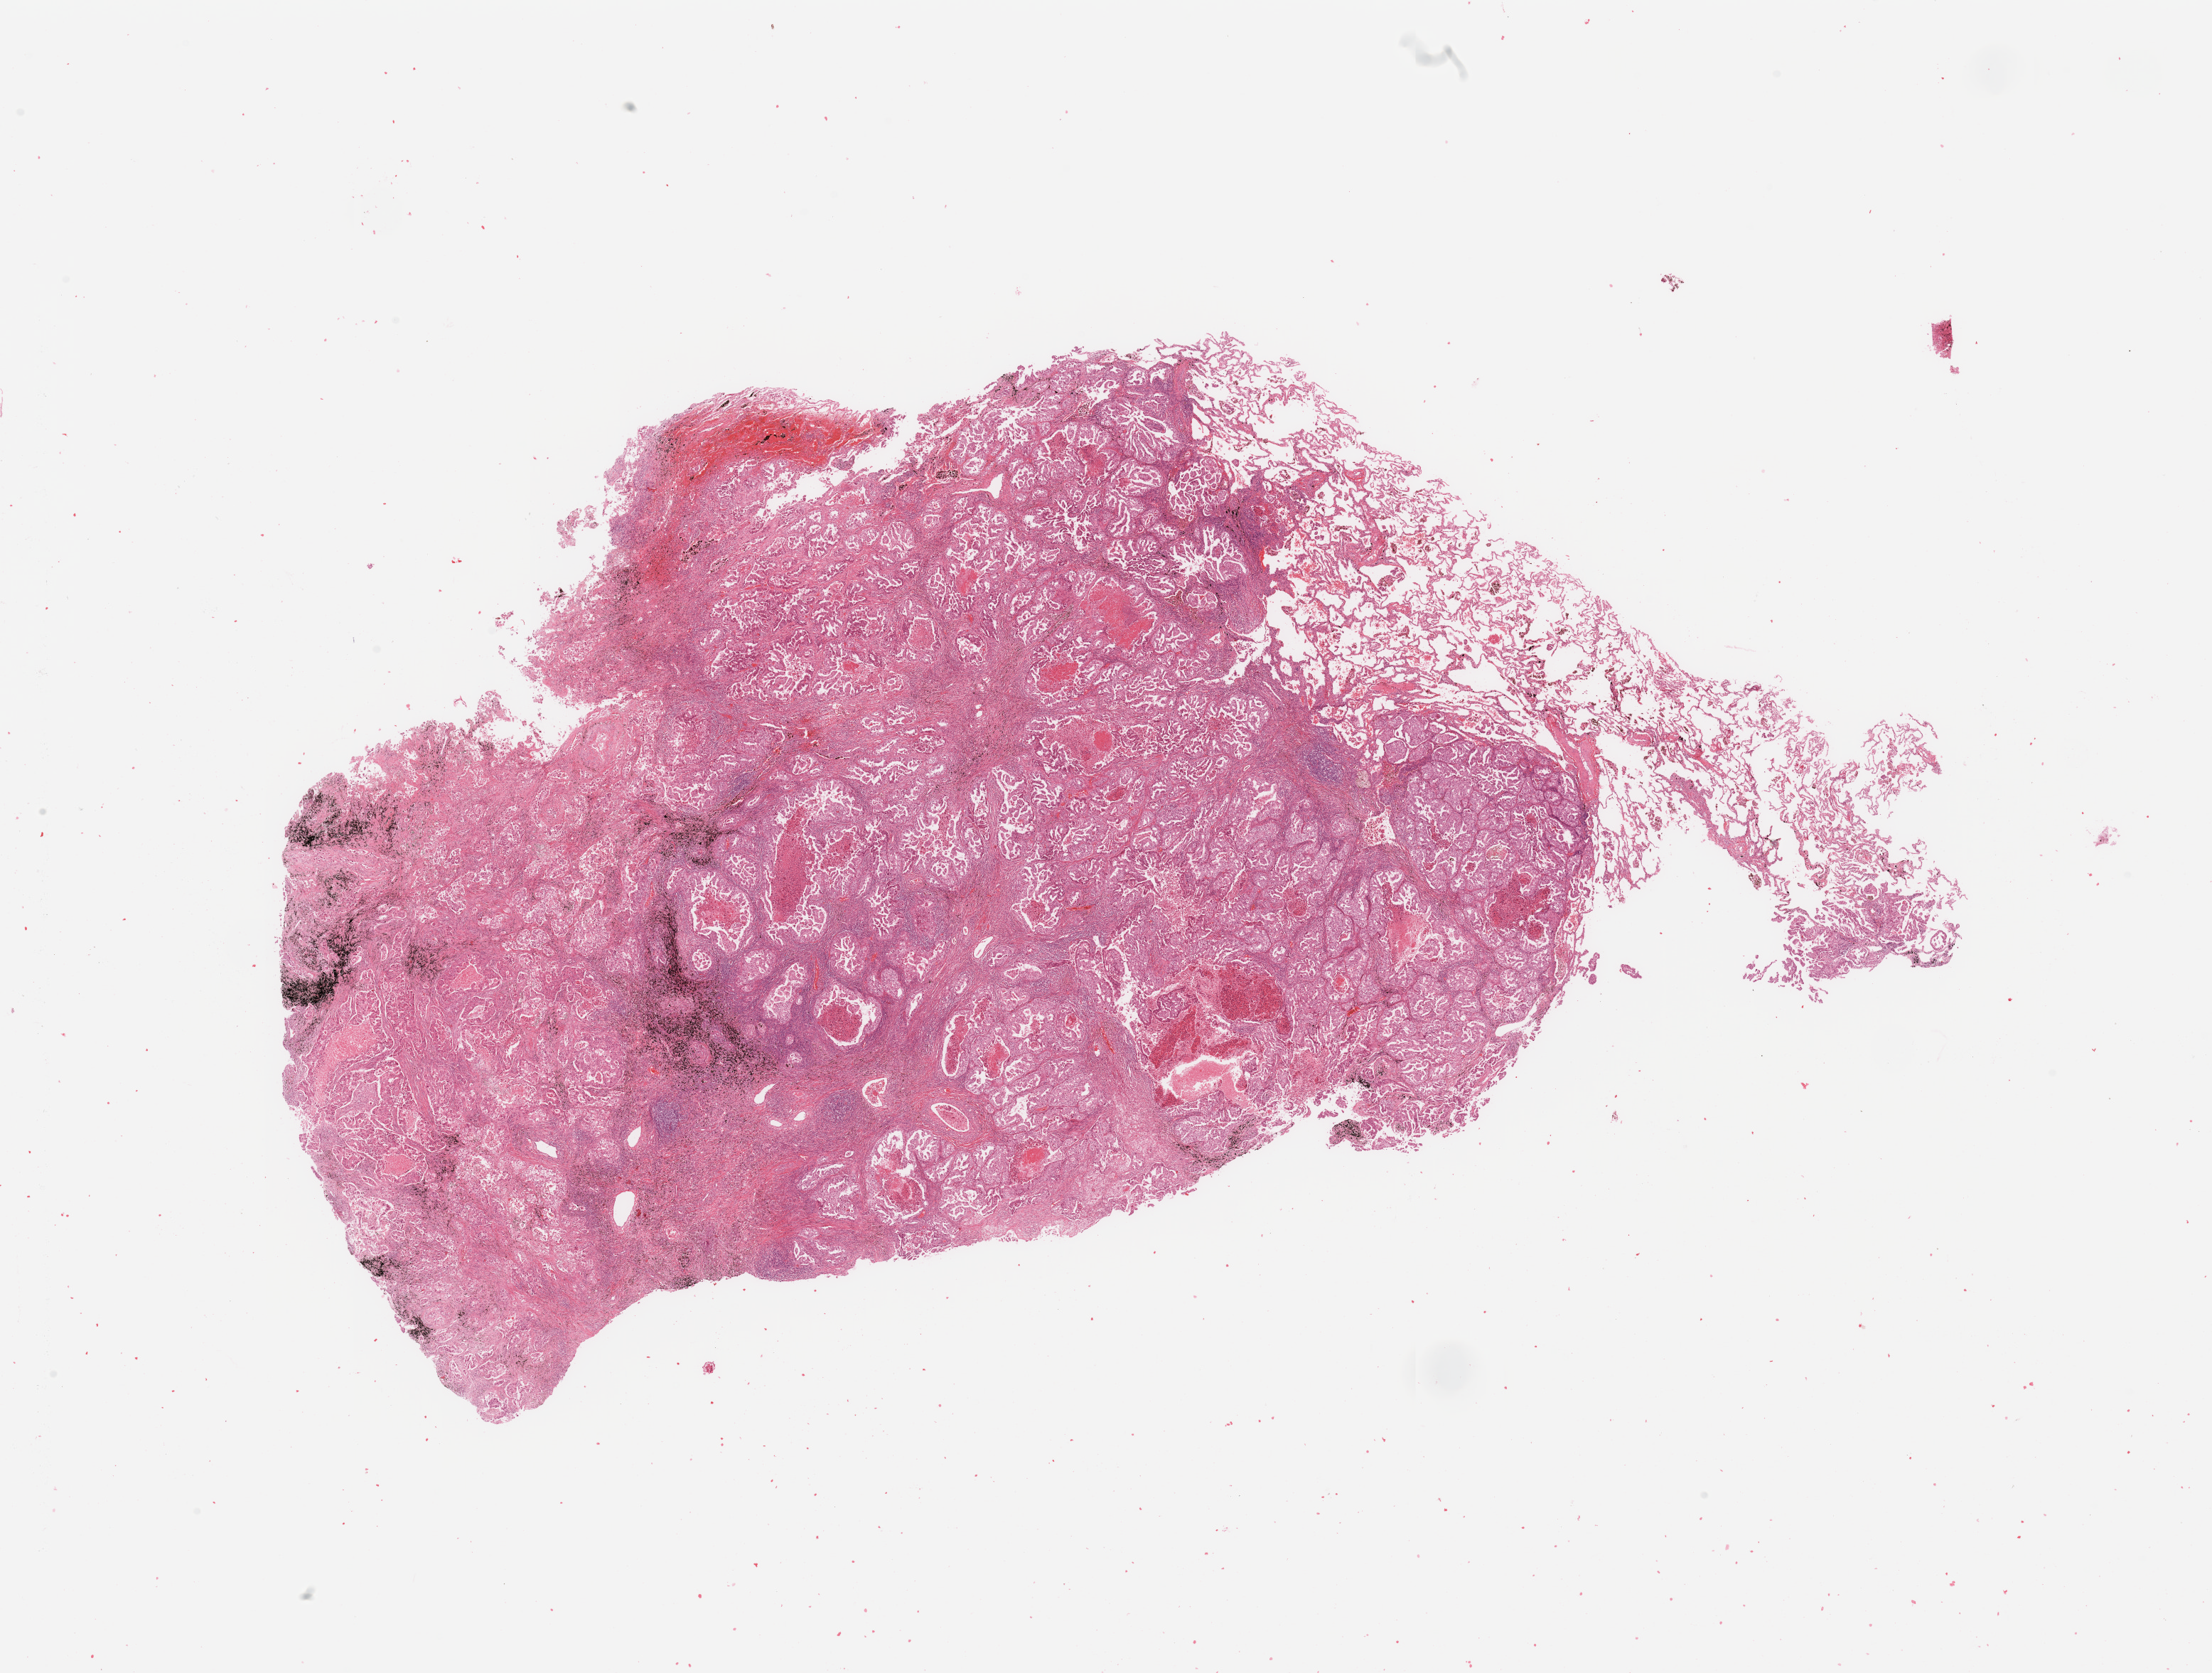
Hematoxylin and eosin (H&E) stained whole-slide image — a low-resolution overview of the entire scanned area, about 24.6 x 18.6 mm (from a 20x scan), lung, tumour tissue. Male, 48 y/o. Histologic grade: G2 (moderately differentiated).
AJCC pathologic stage: IB. Diagnosis: Adenocarcinoma, NOS. Primary tumour site (as recorded): right lower lobe.